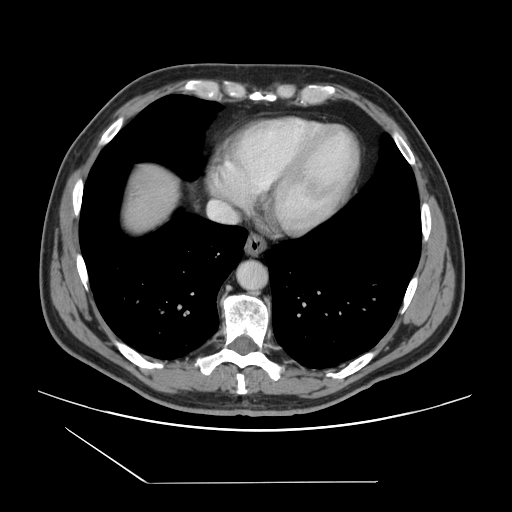
Contrast-enhanced abdominal CT, one axial slice. Slice 138 of 157 in the series (ordered by position). 120 kVp. Intravenous contrast given. Soft-tissue window (W 400 / L 40 HU). 2.5 mm slice thickness. 512 × 512 image matrix. Male patient, age 61 years. Case-level facts recorded for this patient, not image findings: diagnosis: colorectal cancer liver metastases, imaged before liver resection; multiple liver metastases: yes; largest metastasis: 5.5 cm; chemotherapy before resection: no.
Annotated regions visible in this slice (expert manual segmentation):
- liver: bounding box (x1, y1, x2, y2) in pixels: (123, 168, 177, 232)
- planned liver remnant (the part of the liver to remain after resection): (124, 168, 177, 226)